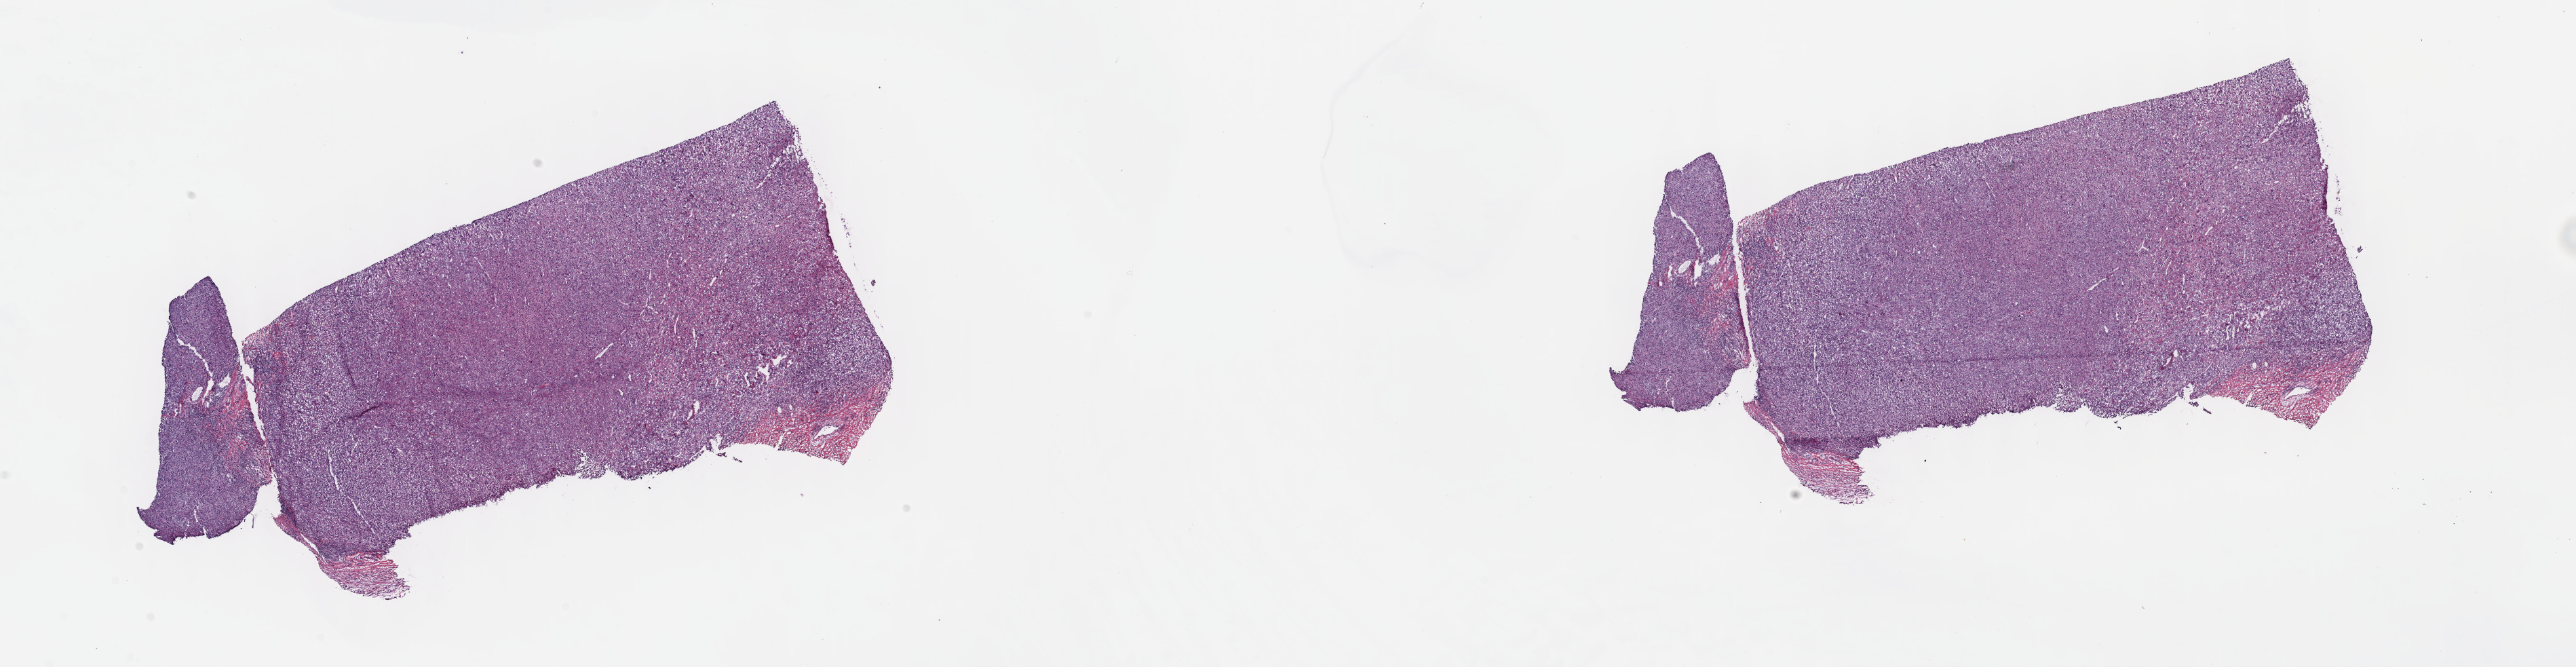
Digitized H&E tissue section (whole slide), shown as a low-resolution overview of the whole scanned area (about 30.7 x 7.9 mm, acquisition: 40x scan), frozen section from the top of the tissue portion, sample: primary tumour, connective, subcutaneous and other soft tissues. Male patient; age at initial diagnosis 85 years. Composition of this section per pathologist review: tumour cells 100%, tumour nuclei 80%, normal cells 0%, stromal cells 0%, necrosis 0%. Infiltration values recorded for this section: lymphocyte infiltration 1%, monocyte infiltration 0%, neutrophil infiltration 0%.
Pathologic diagnosis: Malignant fibrous histiocytoma (connective, subcutaneous and other soft tissues of lower limb and hip).